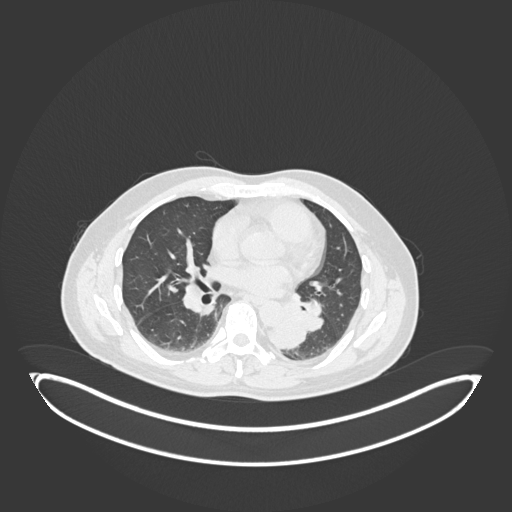
Chest CT, one axial slice; position 93 of 258 along the scan axis; 120 kVp; lung window (W 1500 / L -600 HU); 1 mm slice thickness; 512 × 512 image matrix, field of view 500 × 500 mm. Patient: male, 54 years. Case-level facts recorded for this patient, not image findings: clinical TNM (as recorded): T3 N0 M0.
Annotated regions visible in this slice (bounding box drawn by a radiologist):
- lung tumour (recorded histology: squamous cell carcinoma): bounding box <262,299,309,352> (left, top, right, bottom; pixels)